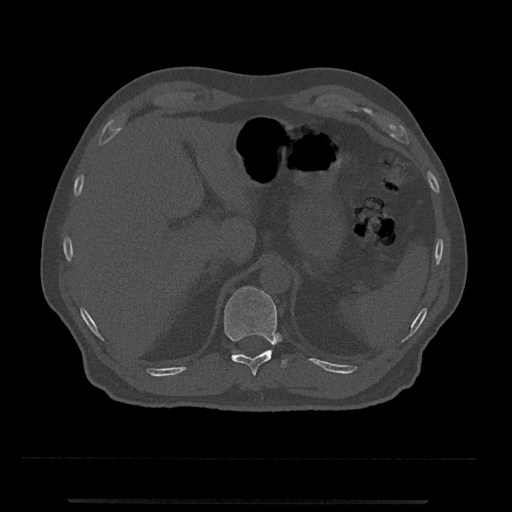
CT including the spine, one axial slice. Reconstruction kernel Br40s/3. 120 kVp. Bone window (W 1800 / L 400 HU). 512 × 512 image matrix. Male patient, age 63 years. From the clinical record (not read from this slice): primary cancer: prostate.
Outlined on this slice (semi-automatically segmented with operator editing):
- T11 vertebra: bounding box <224,286,287,375> (left, top, right, bottom; pixels)
- T12 vertebra: <233,351,235,354>